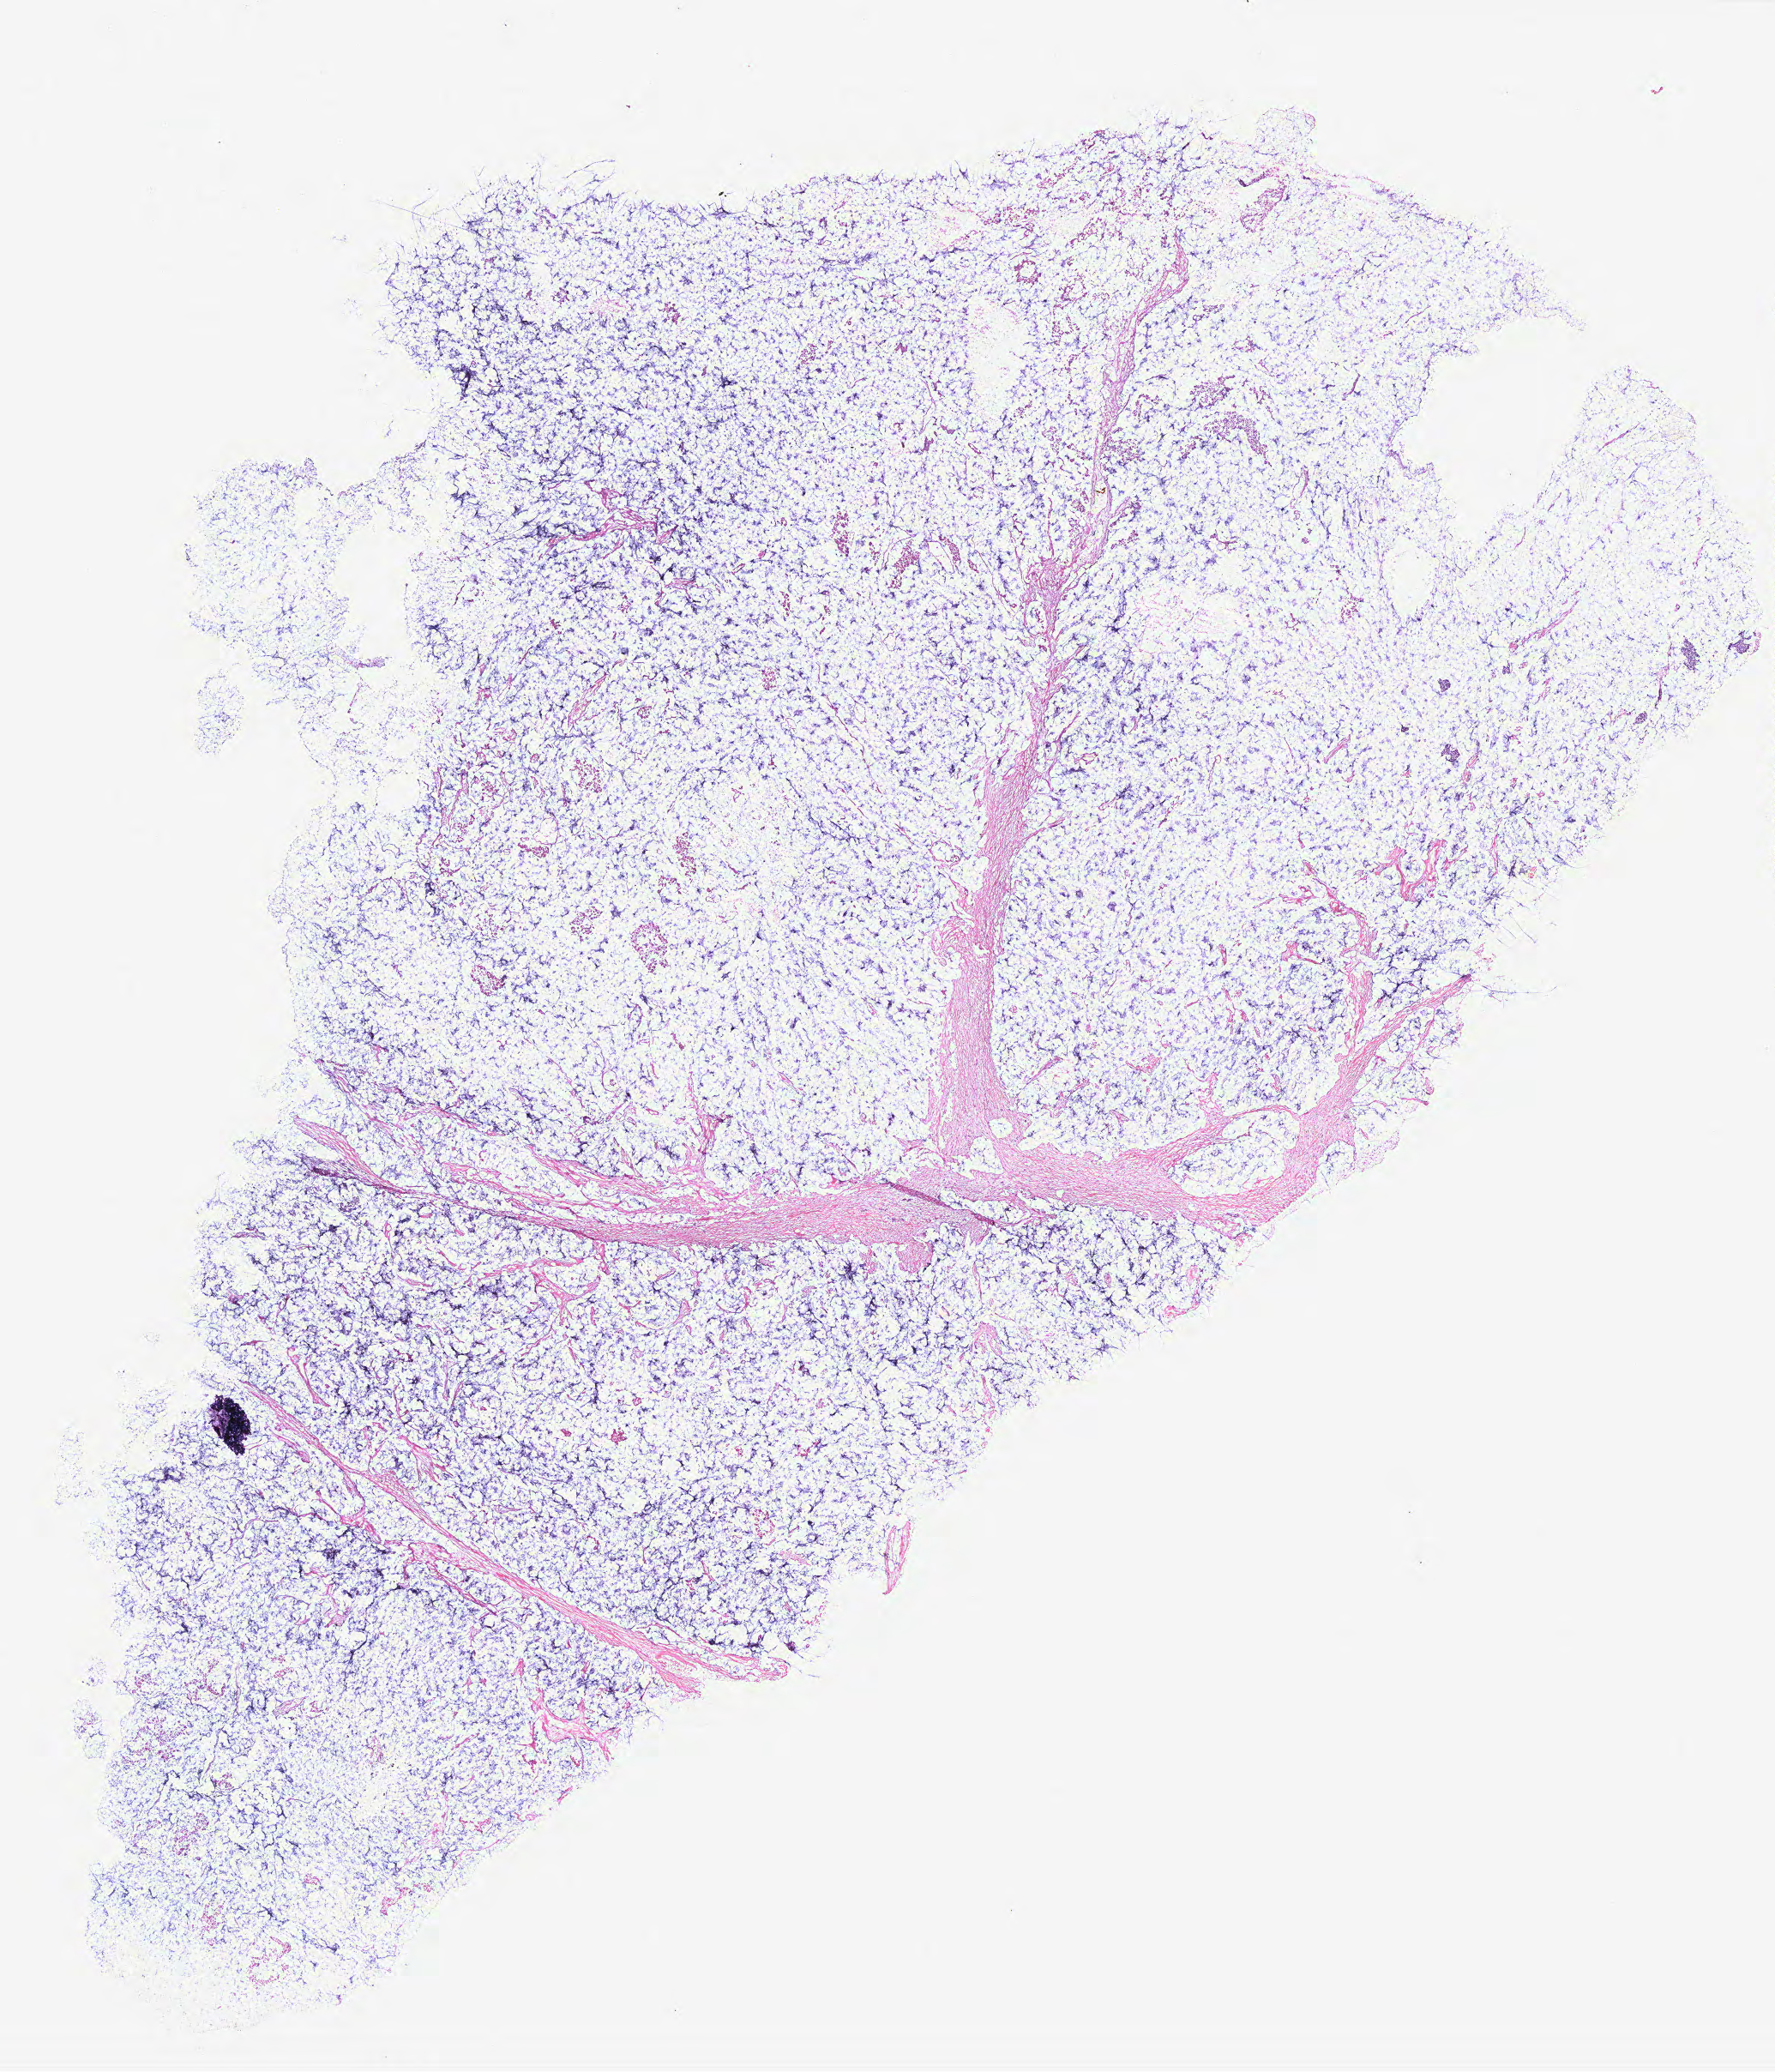
Digitized Hematoxylin and eosin (H&E) stained tissue section (whole slide) — a low-resolution overview of the entire scanned area, about 16.6 x 19.3 mm (from a 40x scan); breast, tissue type not recorded.
Patient diagnosis (cohort enrolment): breast cancer (breast).